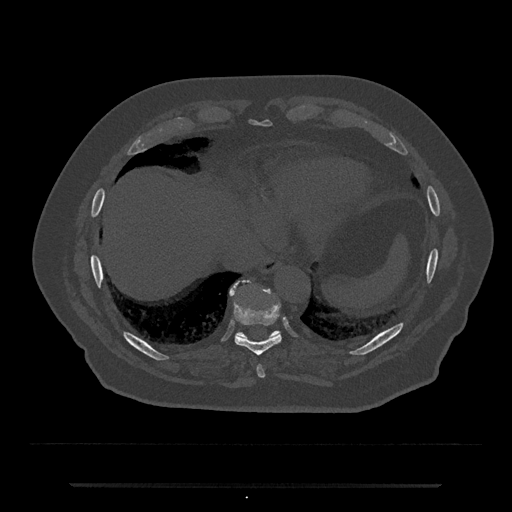
CT including the spine, one axial slice; position 746 of 797 along the scan axis; reconstruction kernel Br40s/3; 120 kVp; bone window (W 1800 / L 400 HU); 0.5 mm slice thickness; 512 × 512 image matrix. Male patient, age 80 years. From the clinical record (not read from this slice): primary cancer: prostate; vertebrae with lytic lesions (as recorded): L1, T11.
Annotated regions visible in this slice (semi-automatically segmented with operator editing):
- T10 vertebra: bounding box <230,281,281,339> (left, top, right, bottom; pixels)
- T8 vertebra: <257,365,265,378>
- T9 vertebra: <235,306,282,356>